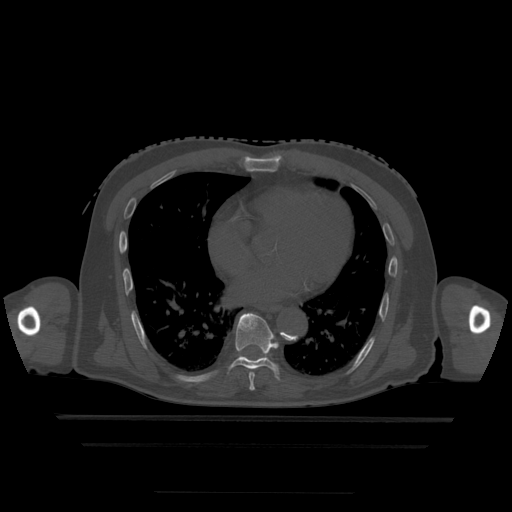
CT including the spine, one axial slice; position 281 of 522 along the scan axis; bone window (W 1800 / L 400 HU); 1.25 mm slice thickness; 512 × 512 image matrix, field of view 436 × 436 mm. Patient age 68 years. Case-level facts recorded for this patient, not image findings: primary cancer: urothelial.
Outlined on this slice (semi-automatic segmentation, software-assisted and operator-edited):
- T7 vertebra: bounding box [x1, y1, x2, y2] px = [249, 373, 255, 393]
- T8 vertebra: [230, 313, 279, 379]